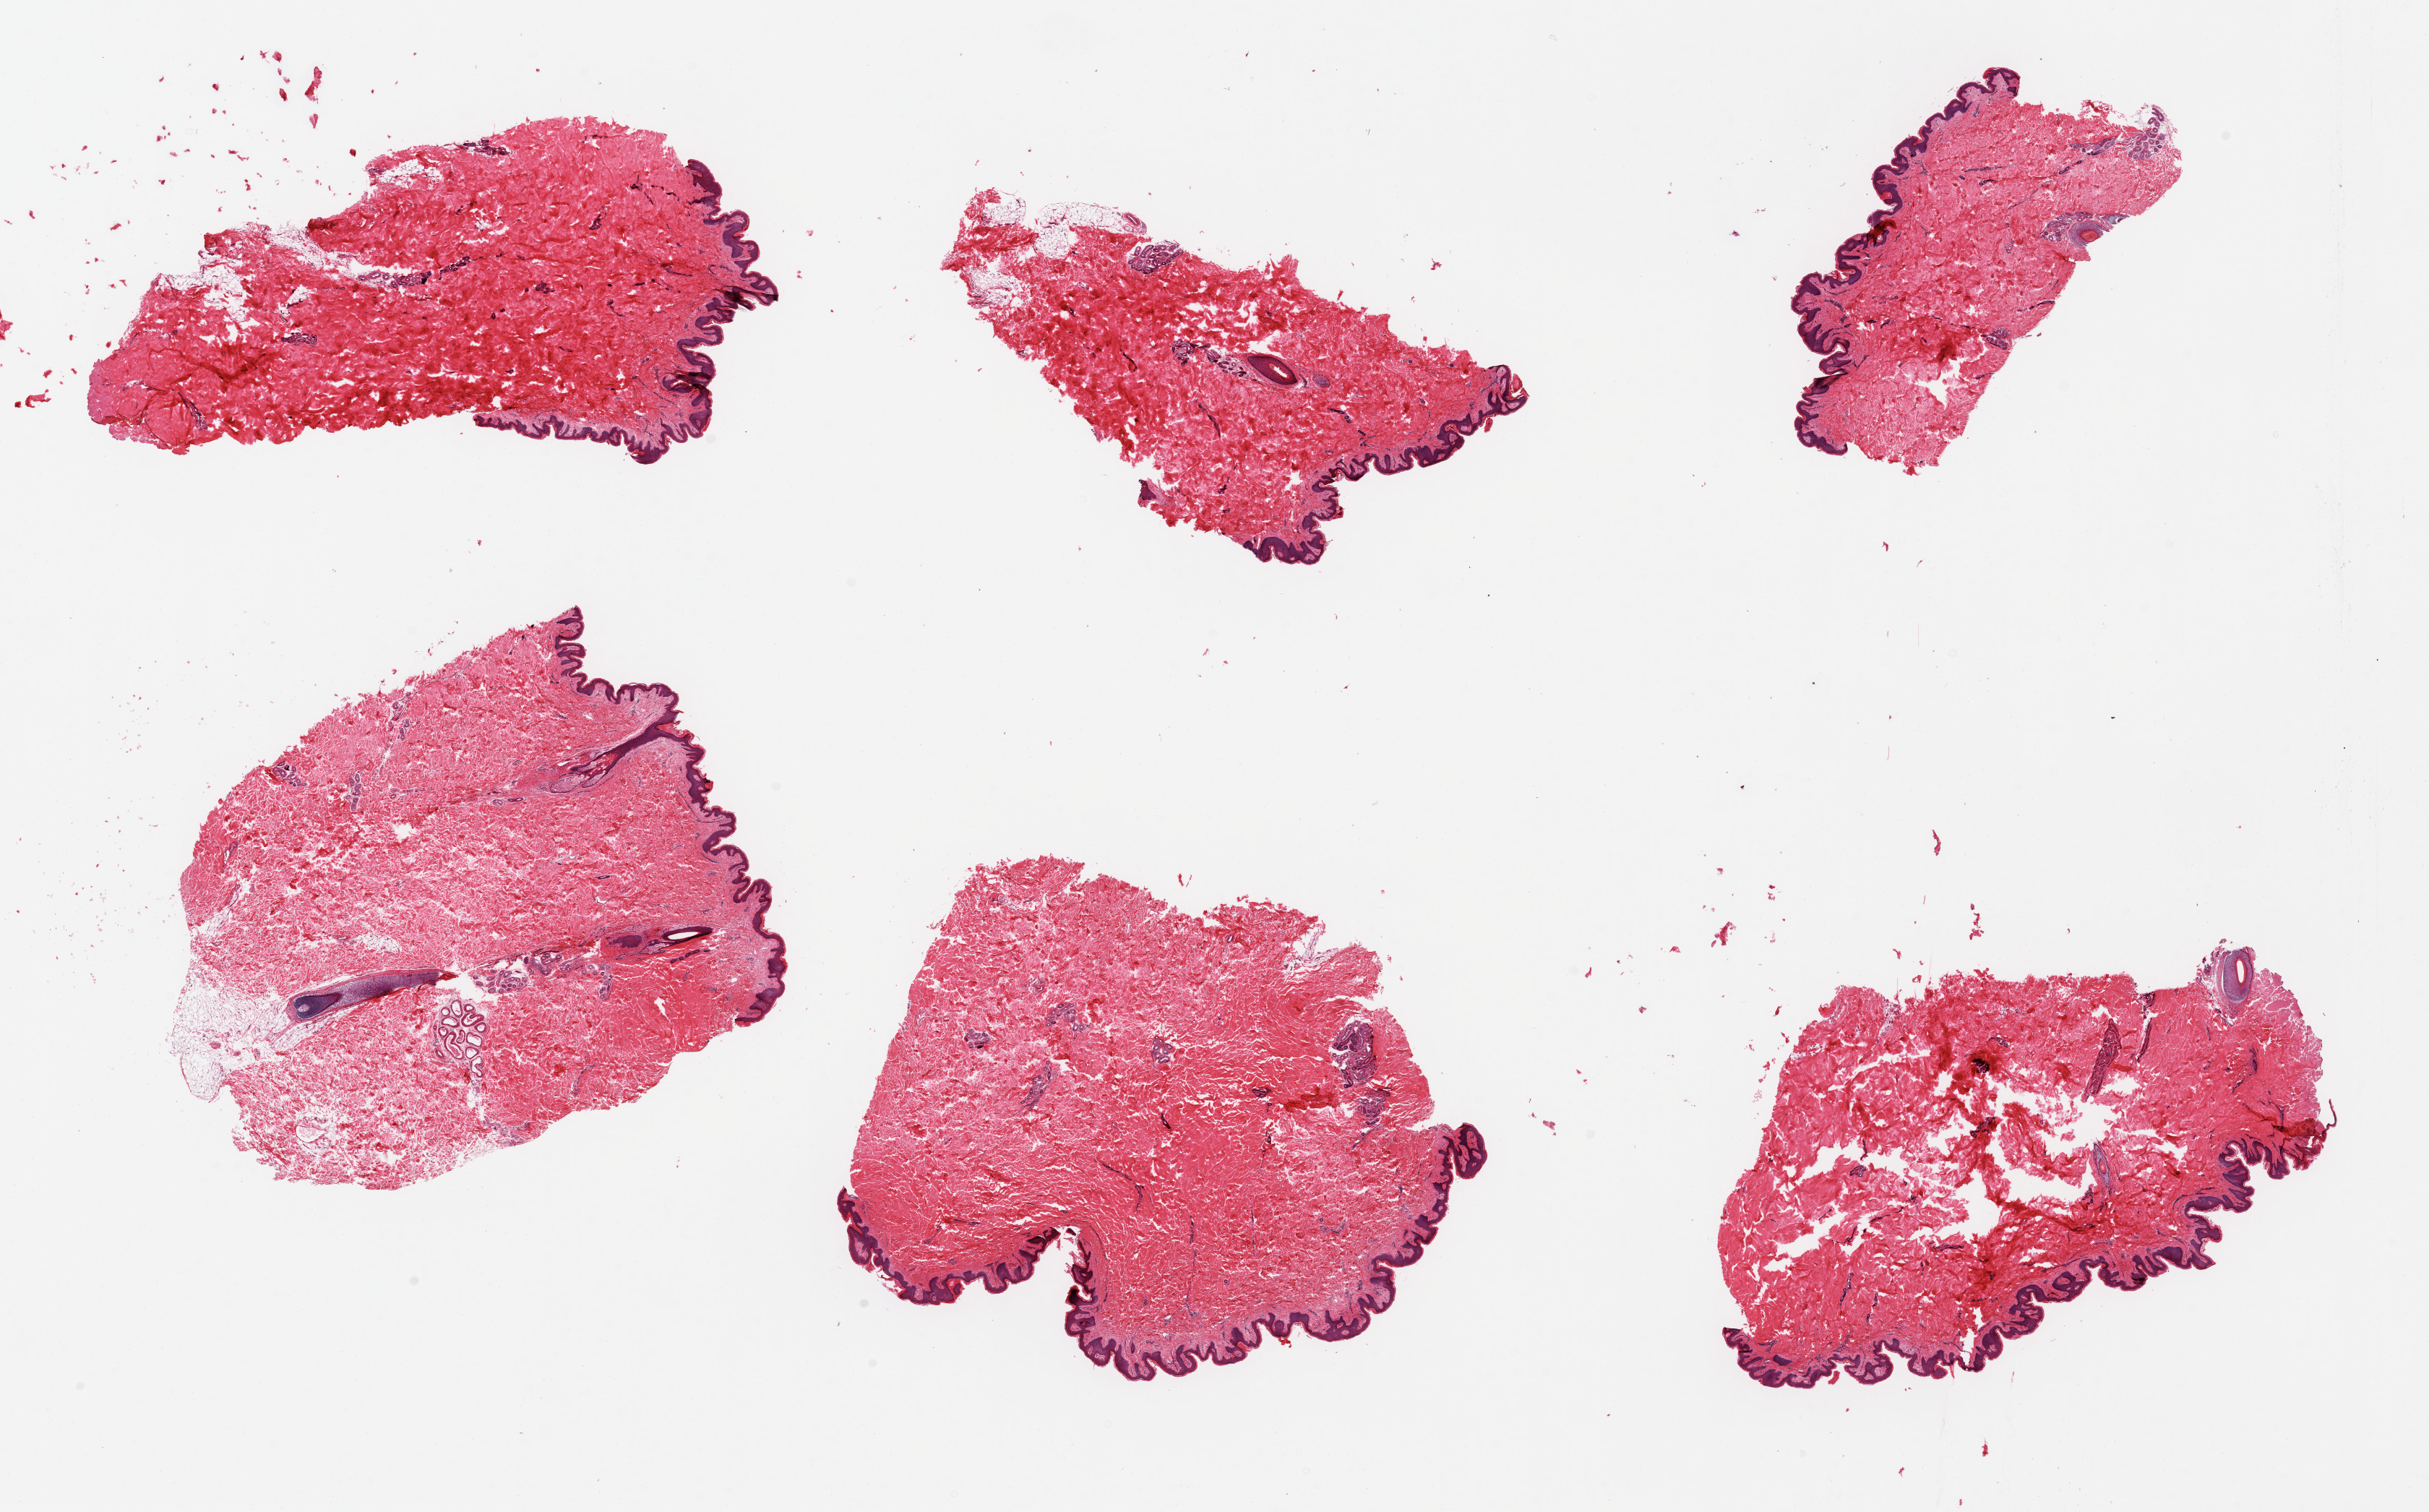
Haematoxylin and eosin whole-slide image, brightfield, a low-resolution overview of the entire scanned area, about 26.6 x 16.5 mm (acquisition: 20x scan); PAXgene-fixed, paraffin-embedded tissue; sampled site (target tissue): skin of suprapubic region; tissue donor sample. Male donor.
- reviewer comment on this tissue sample: 6 pieces; well trimmed; 5% dermal fat